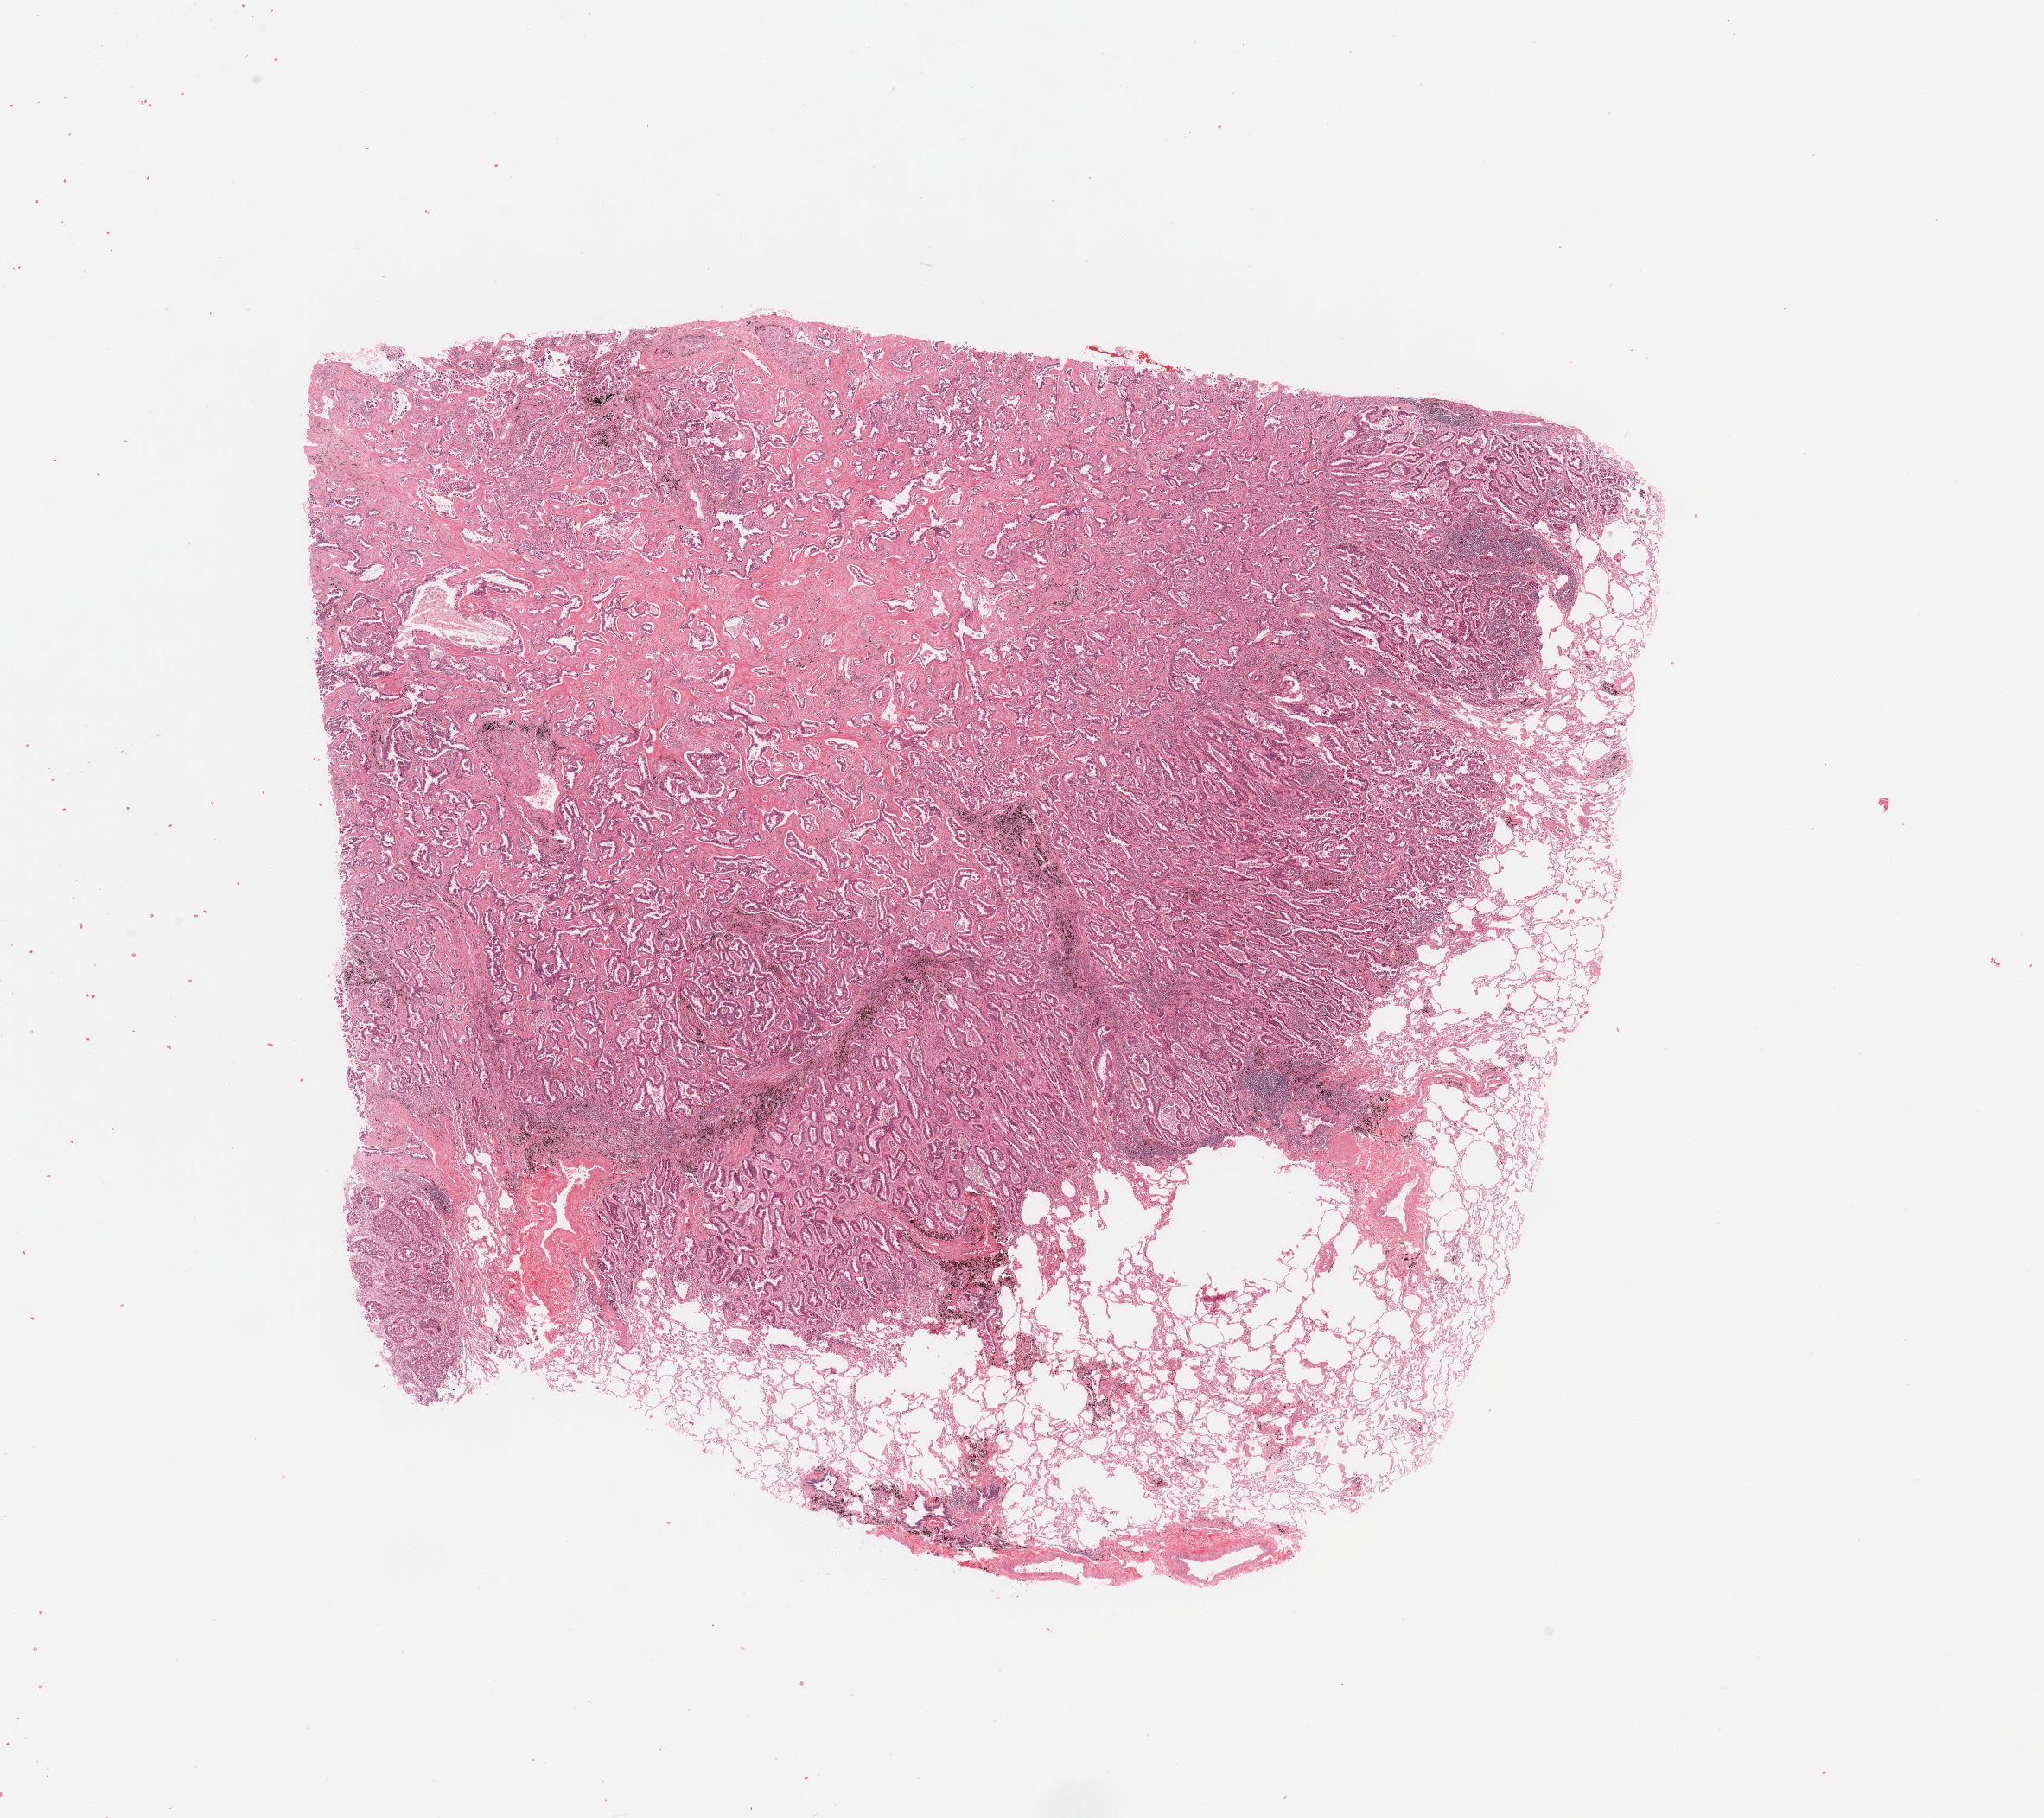
Whole-slide histology image, H&E, low-resolution overview of the scanned area, about 18.7 x 16.6 mm (from a 20x scan), tumour tissue sample, lung. 55-year-old female patient. Histologic grade: G2 (moderately differentiated).
- AJCC pathologic stage: IA
- diagnosis: Adenocarcinoma, NOS